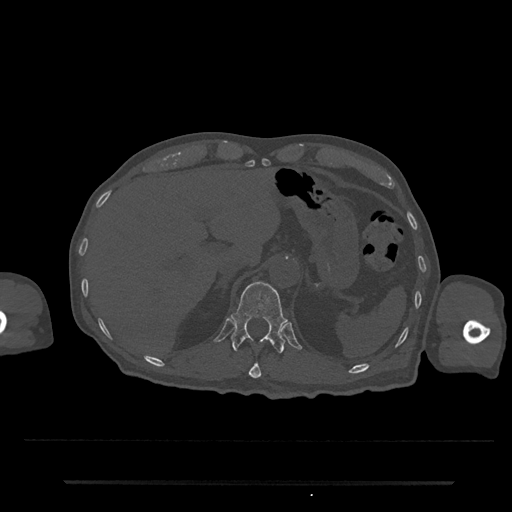
CT including the spine, one axial slice; slice 210 of 797 in the series (ordered by position); bone window (W 1800 / L 400 HU); 512 × 512 image matrix, field of view 427 × 427 mm. Patient: male, 74 years. Case-level facts recorded for this patient, not image findings: primary cancer: prostate.
Outlined on this slice (semi-automatically segmented with operator editing):
- T11 vertebra: bounding box (x1, y1, x2, y2) in pixels: (249, 361, 261, 379)
- T12 vertebra: (231, 281, 287, 354)